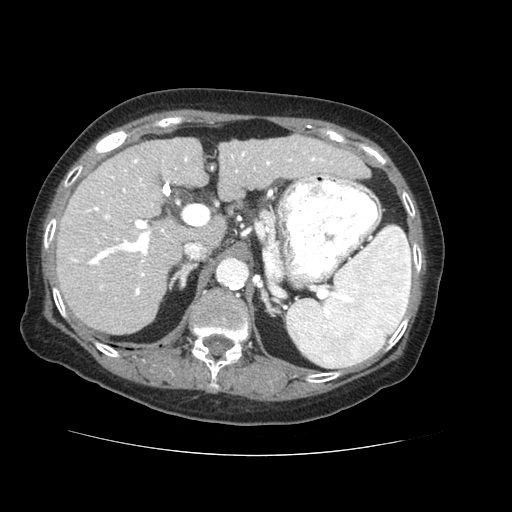
Contrast-enhanced abdominal CT (liver protocol), one axial slice. Slice 37 of 73 in the series (ordered by position). Reconstruction kernel STANDARD. 120 kVp. Soft-tissue window (W 400 / L 40 HU). 2.5 mm slice thickness. 512 × 512 image matrix, field of view 360 × 360 mm. Case-level facts recorded for this patient, not image findings: diagnosis: hepatocellular carcinoma (patient treated with transarterial chemoembolisation; whether this scan precedes or follows treatment is not stated here); TNM stage (as recorded): Stage-IVB; Child-Pugh class: A; tumour differentiation: well differentiated.
Annotated regions visible in this slice (semi-automatically segmented with operator editing):
- liver parenchyma outside the tumour (the mass and vessels are separate outlines, so this box may not span the whole liver): bounding box [x1, y1, x2, y2] px = [56, 136, 370, 334]
- liver vessels: [71, 144, 333, 296]